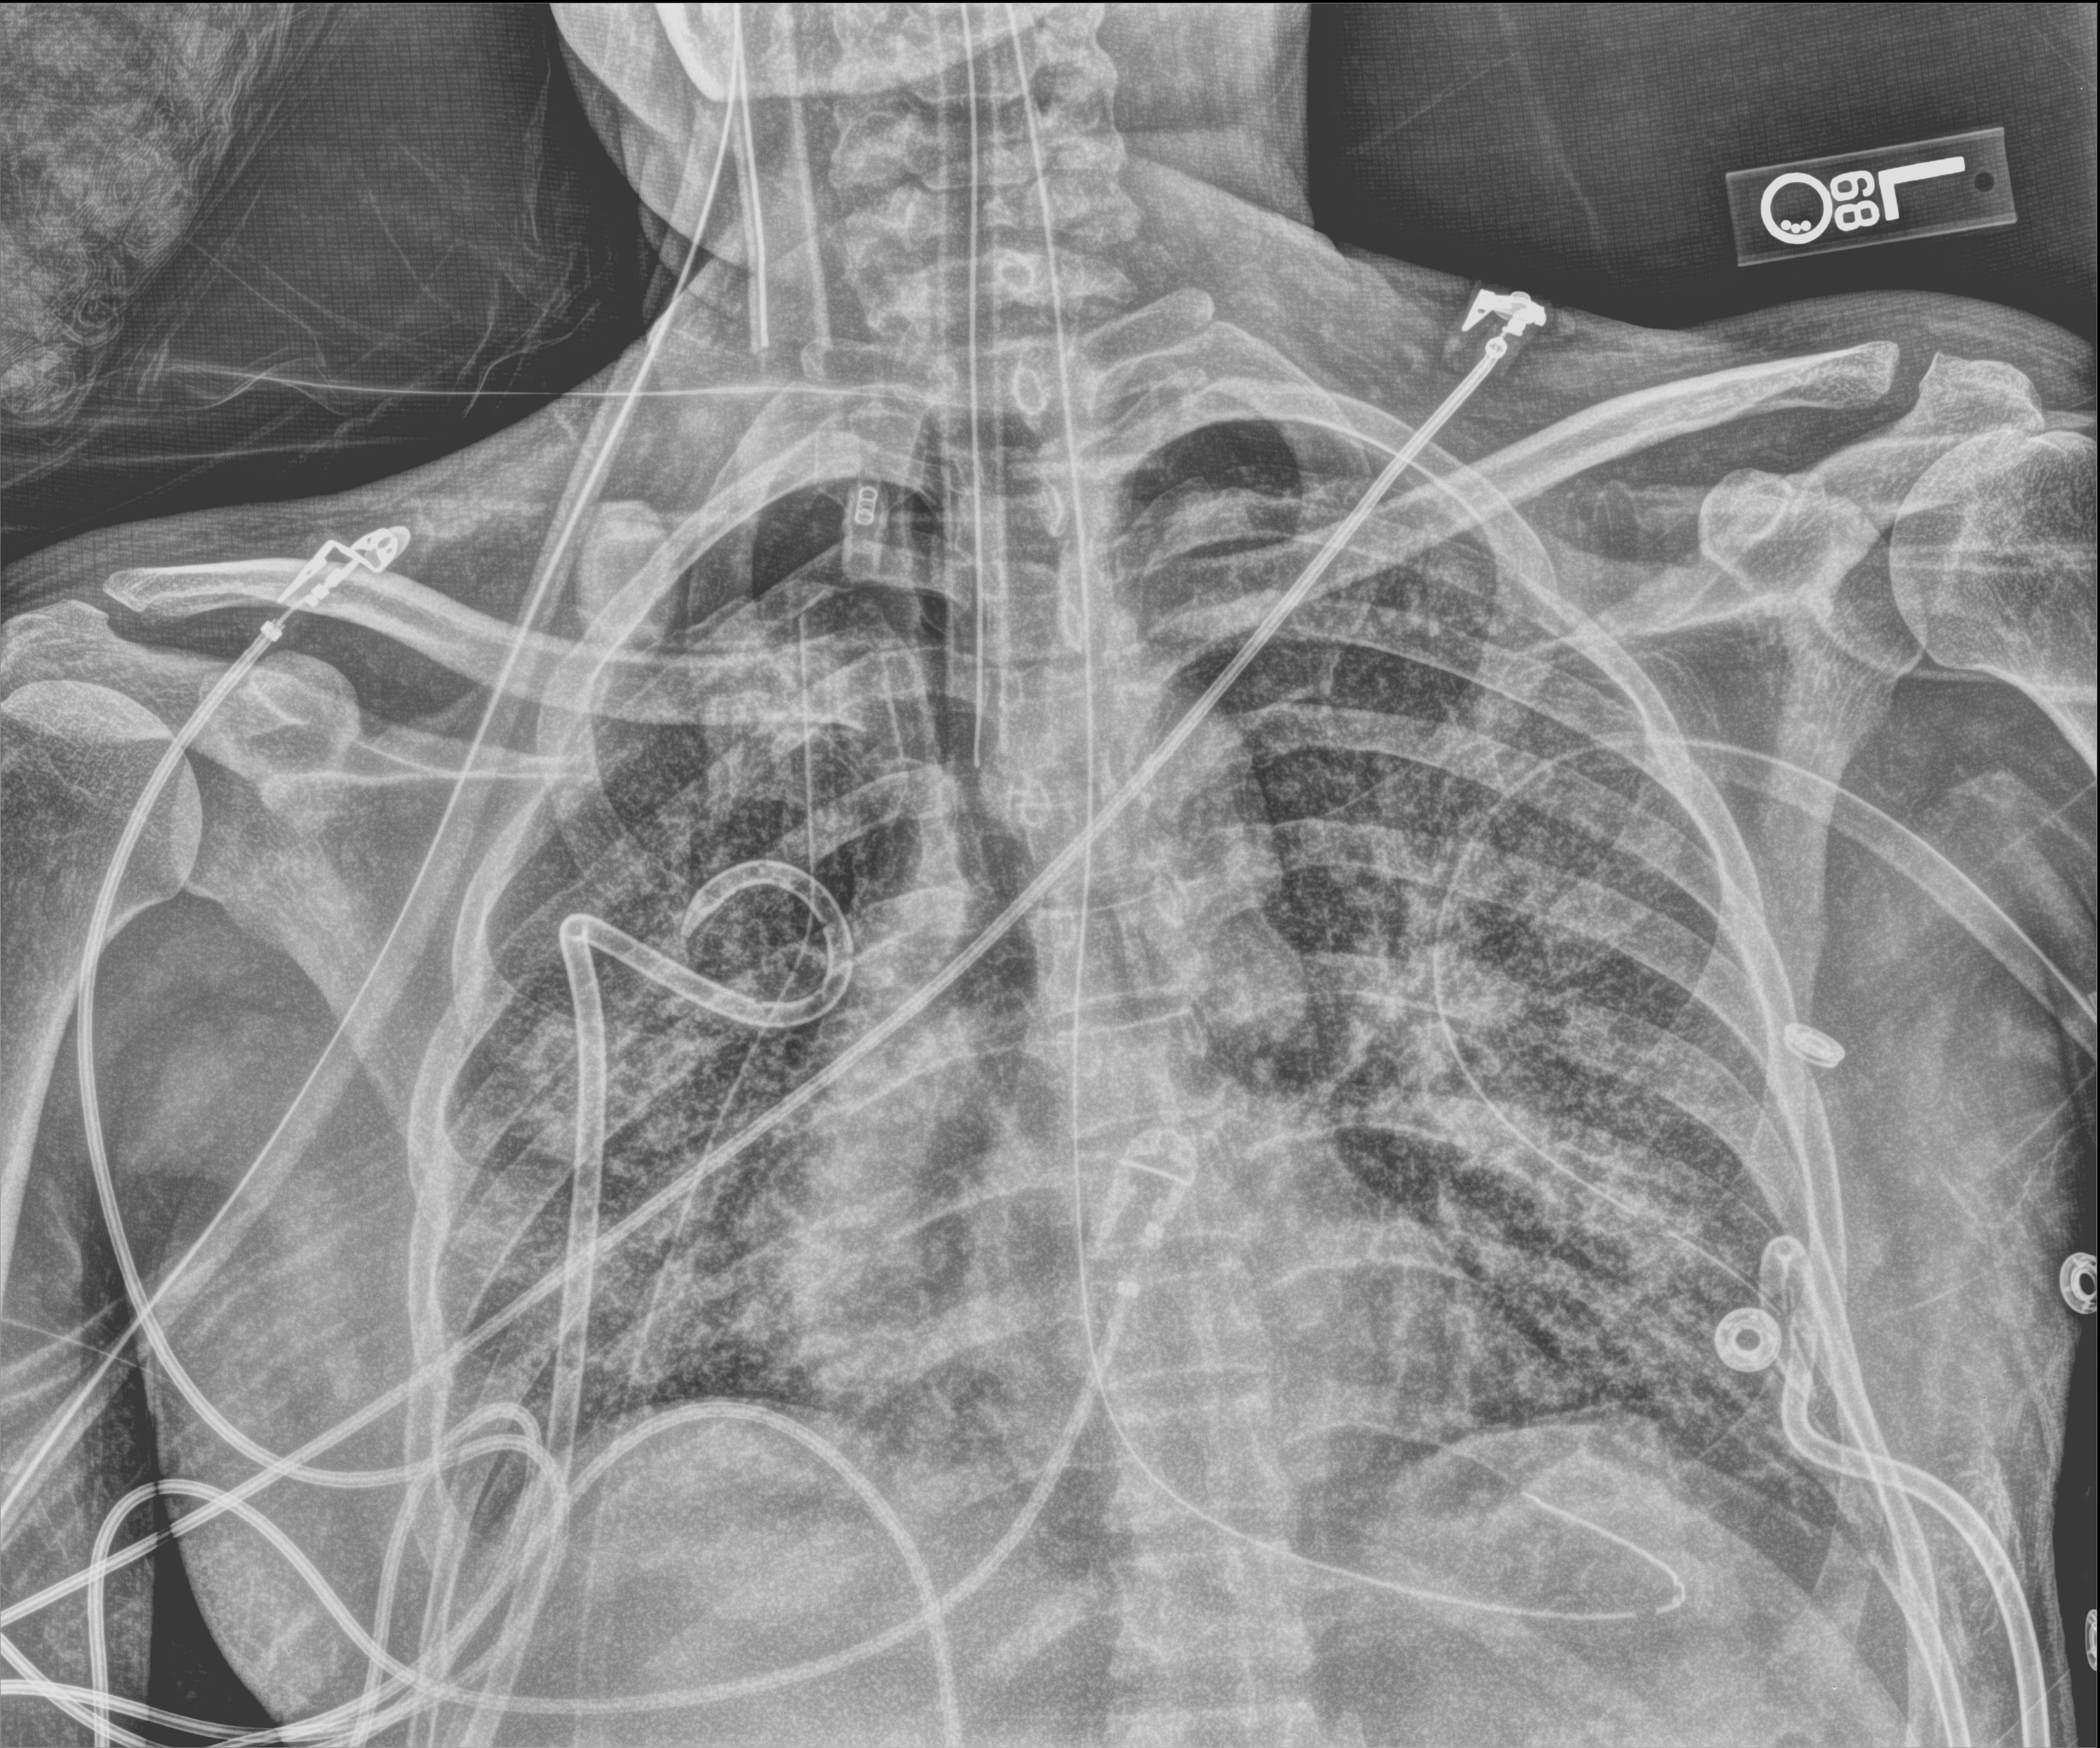
Portable chest radiograph, anteroposterior (AP) projection. Adult patient hospitalised with COVID-19, age 18–59 years.
From the hospital-stay record, not from the radiograph (when in the stay this image was taken is not recorded): chronic kidney disease (admission record): no.